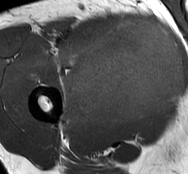
MRI of an extremity soft-tissue mass, one axial slice; position 44 of 93 along the scan axis; MR volume resampled by the dataset authors to the PET/CT grid (not the native acquisition matrix); 3.27 mm slice thickness; 188 × 174 image matrix, field of view 184 × 170 mm. Male patient. From the clinical record (not read from this slice): histological type: undifferentiated - pleiomorphic; grade: high; site of the primary tumour: right thigh.
Annotated regions visible in this slice (expert contour drawn on MRI and transferred to this co-registered scan by the dataset authors):
- gross tumour volume including surrounding oedema: bounding box (x1, y1, x2, y2) in pixels: (59, 17, 183, 129)
- gross tumour volume (mass): (70, 19, 183, 125)